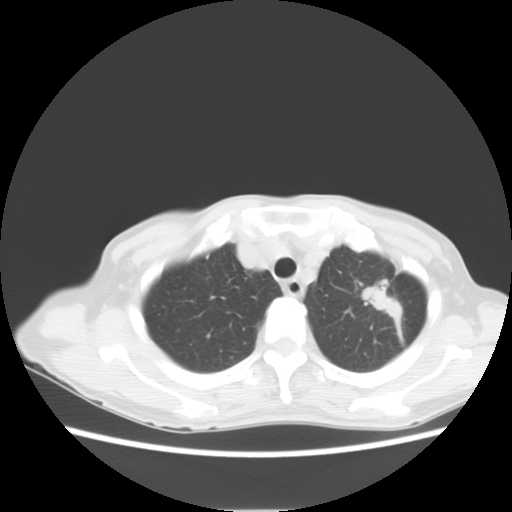
Chest CT, one axial slice. Position 11 of 14 along the scan axis. Lung window (W 1500 / L -600 HU). 5 mm slice thickness. 512 × 512 image matrix, field of view 350 × 350 mm. Female patient, age 71 years. From the clinical record (not read from this slice): clinical TNM (as recorded): T2 N0 M0.
Structures marked on this image (rectangle marked by the reading radiologist):
- lung tumour (recorded histology: adenocarcinoma): bounding box (x1, y1, x2, y2) in pixels: (359, 279, 407, 324)